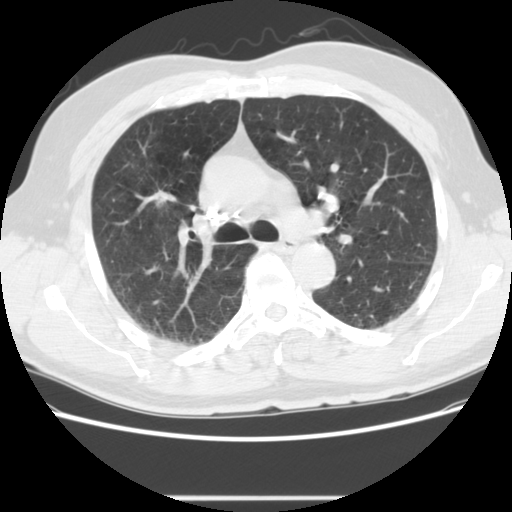
Chest CT (low-dose screening protocol), one axial image. Second annual screen. Lung window (W 1500 / L -600 HU). 2.5 mm slice thickness. Standard (soft-tissue) reconstruction kernel (STANDARD). Slice 51 of 139 in the series. 512 × 512 image matrix. Male participant, aged 59 years at enrolment. Current smoker at enrolment.
Expert-annotated lung lesion, bounding box [x1, y1, x2, y2] px = [139, 182, 180, 220]. Reader record for this screening exam (exam-level; its link to the box is not recorded): non-calcified nodule or mass ≥4 mm, right upper lobe, 20 × 13 mm, spiculated (stellate) margins, soft tissue attenuation, pre-existing on the prior screen: yes; interval growth: yes. Later outcome: lung cancer diagnosed 267 days after this screen — large cell carcinoma, NOS, right upper lobe, poorly differentiated (G3), stage IIIA (AJCC 6th edition), 34 mm at pathology.